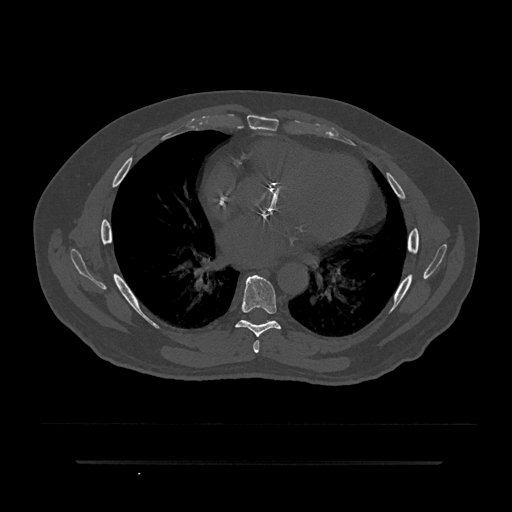
CT including the spine, one axial slice. Position 477 of 797 along the scan axis. Reconstruction kernel Br40s/3. 120 kVp. Bone window (W 1800 / L 400 HU). 0.5 mm slice thickness. 512 × 512 image matrix, field of view 464 × 464 mm. Patient: male, 59 years. Case-level facts recorded for this patient, not image findings: primary cancer: bile ducts; vertebrae with lytic lesions (as recorded): T10.
Annotated regions visible in this slice (semi-automatic segmentation, software-assisted and operator-edited):
- T6 vertebra: bounding box [x1, y1, x2, y2] px = [253, 340, 260, 353]
- T7 vertebra: [235, 275, 281, 337]